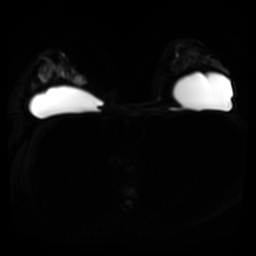
Breast MRI, one axial slice; slice 27 of 45 in the series (ordered by position); diffusion-weighted series; image 2 of 4 stored at this slice position (different b-values; order by instance number); 3 T; 5 mm slice thickness; 256 × 256 image matrix, field of view 320 × 320 mm. Female patient.
Annotated regions visible in this slice (expert manual segmentation):
- tumour on diffusion-weighted imaging: bounding box [x1, y1, x2, y2] px = [74, 77, 85, 84]